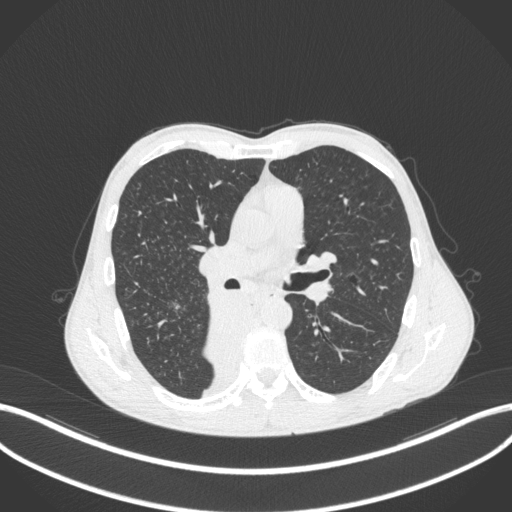
Chest CT, one axial slice. Slice 217 of 371 in the series (ordered by position). Reconstruction kernel B31f. 120 kVp. Lung window (W 1500 / L -600 HU). 1 mm slice thickness. 512 × 512 image matrix, field of view 400 × 400 mm. Male patient, age 58 years. Case-level facts recorded for this patient, not image findings: clinical TNM (as recorded): T3 N1 M1.
Structures marked on this image (rectangle marked by the reading radiologist):
- lung tumour (recorded histology: squamous cell carcinoma): bounding box [x1, y1, x2, y2] px = [205, 291, 264, 379]